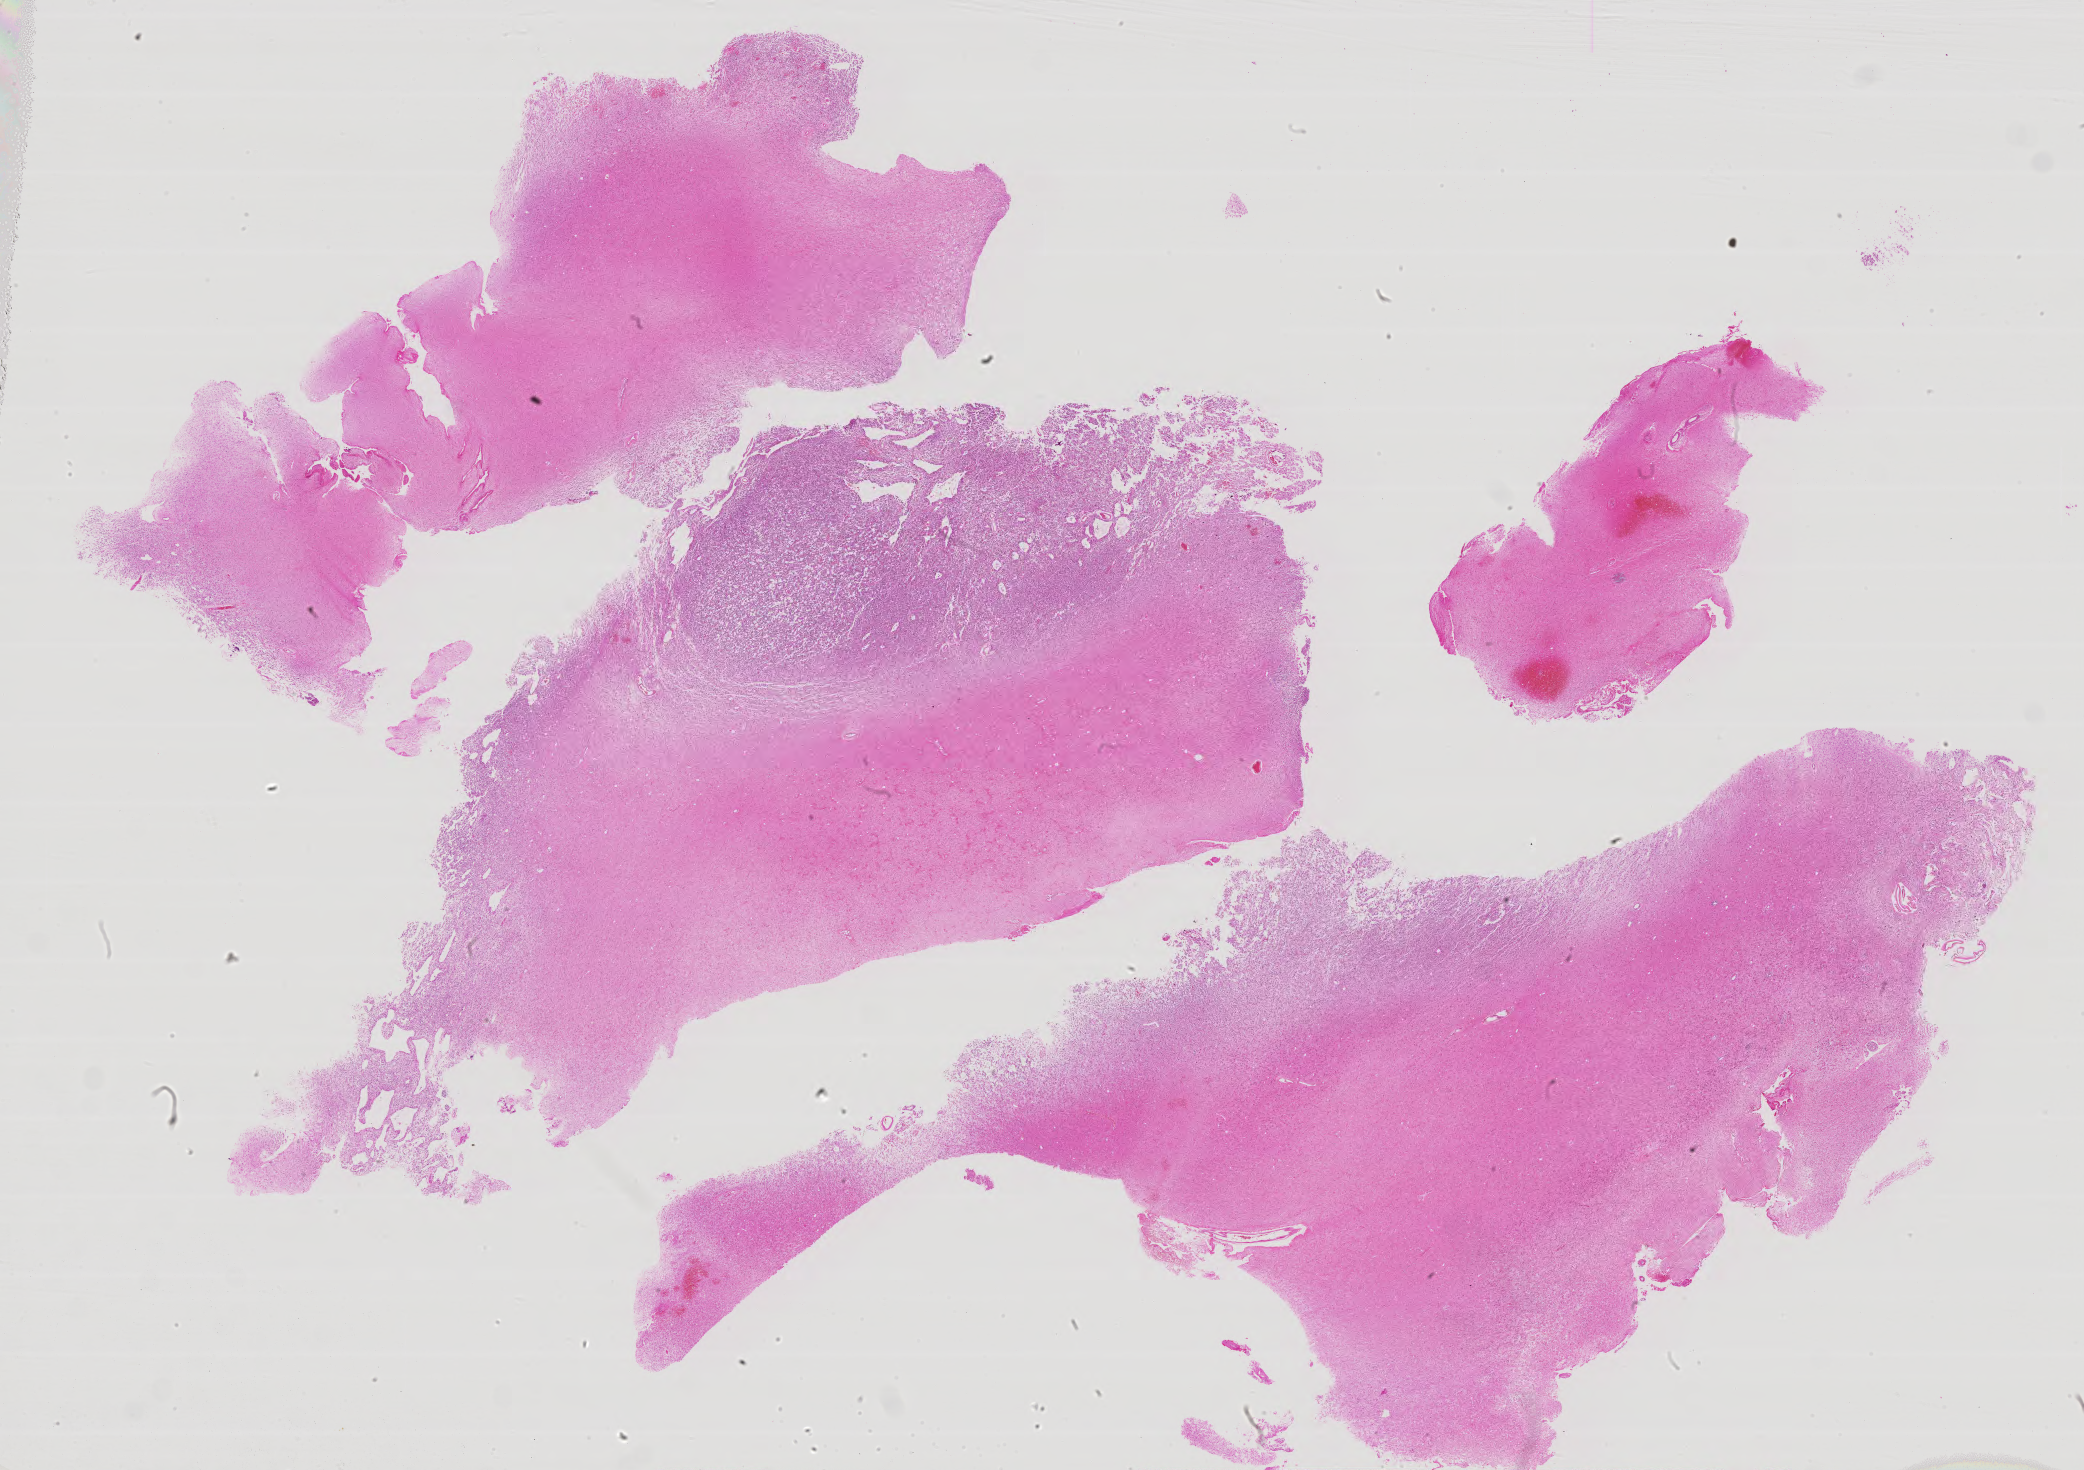
Hematoxylin and eosin (H&E) stained whole-slide image — whole scanned area (about 33.4 x 23.5 mm, from a 40x scan) shown as a low-resolution overview, formalin-fixed paraffin-embedded (FFPE) diagnostic section, brain, primary tumour sample. Male patient; age at initial diagnosis 35 years. Histologic grade: G2 (moderately differentiated).
- laterality: left
- diagnosis: Astrocytoma, NOS (cerebrum)